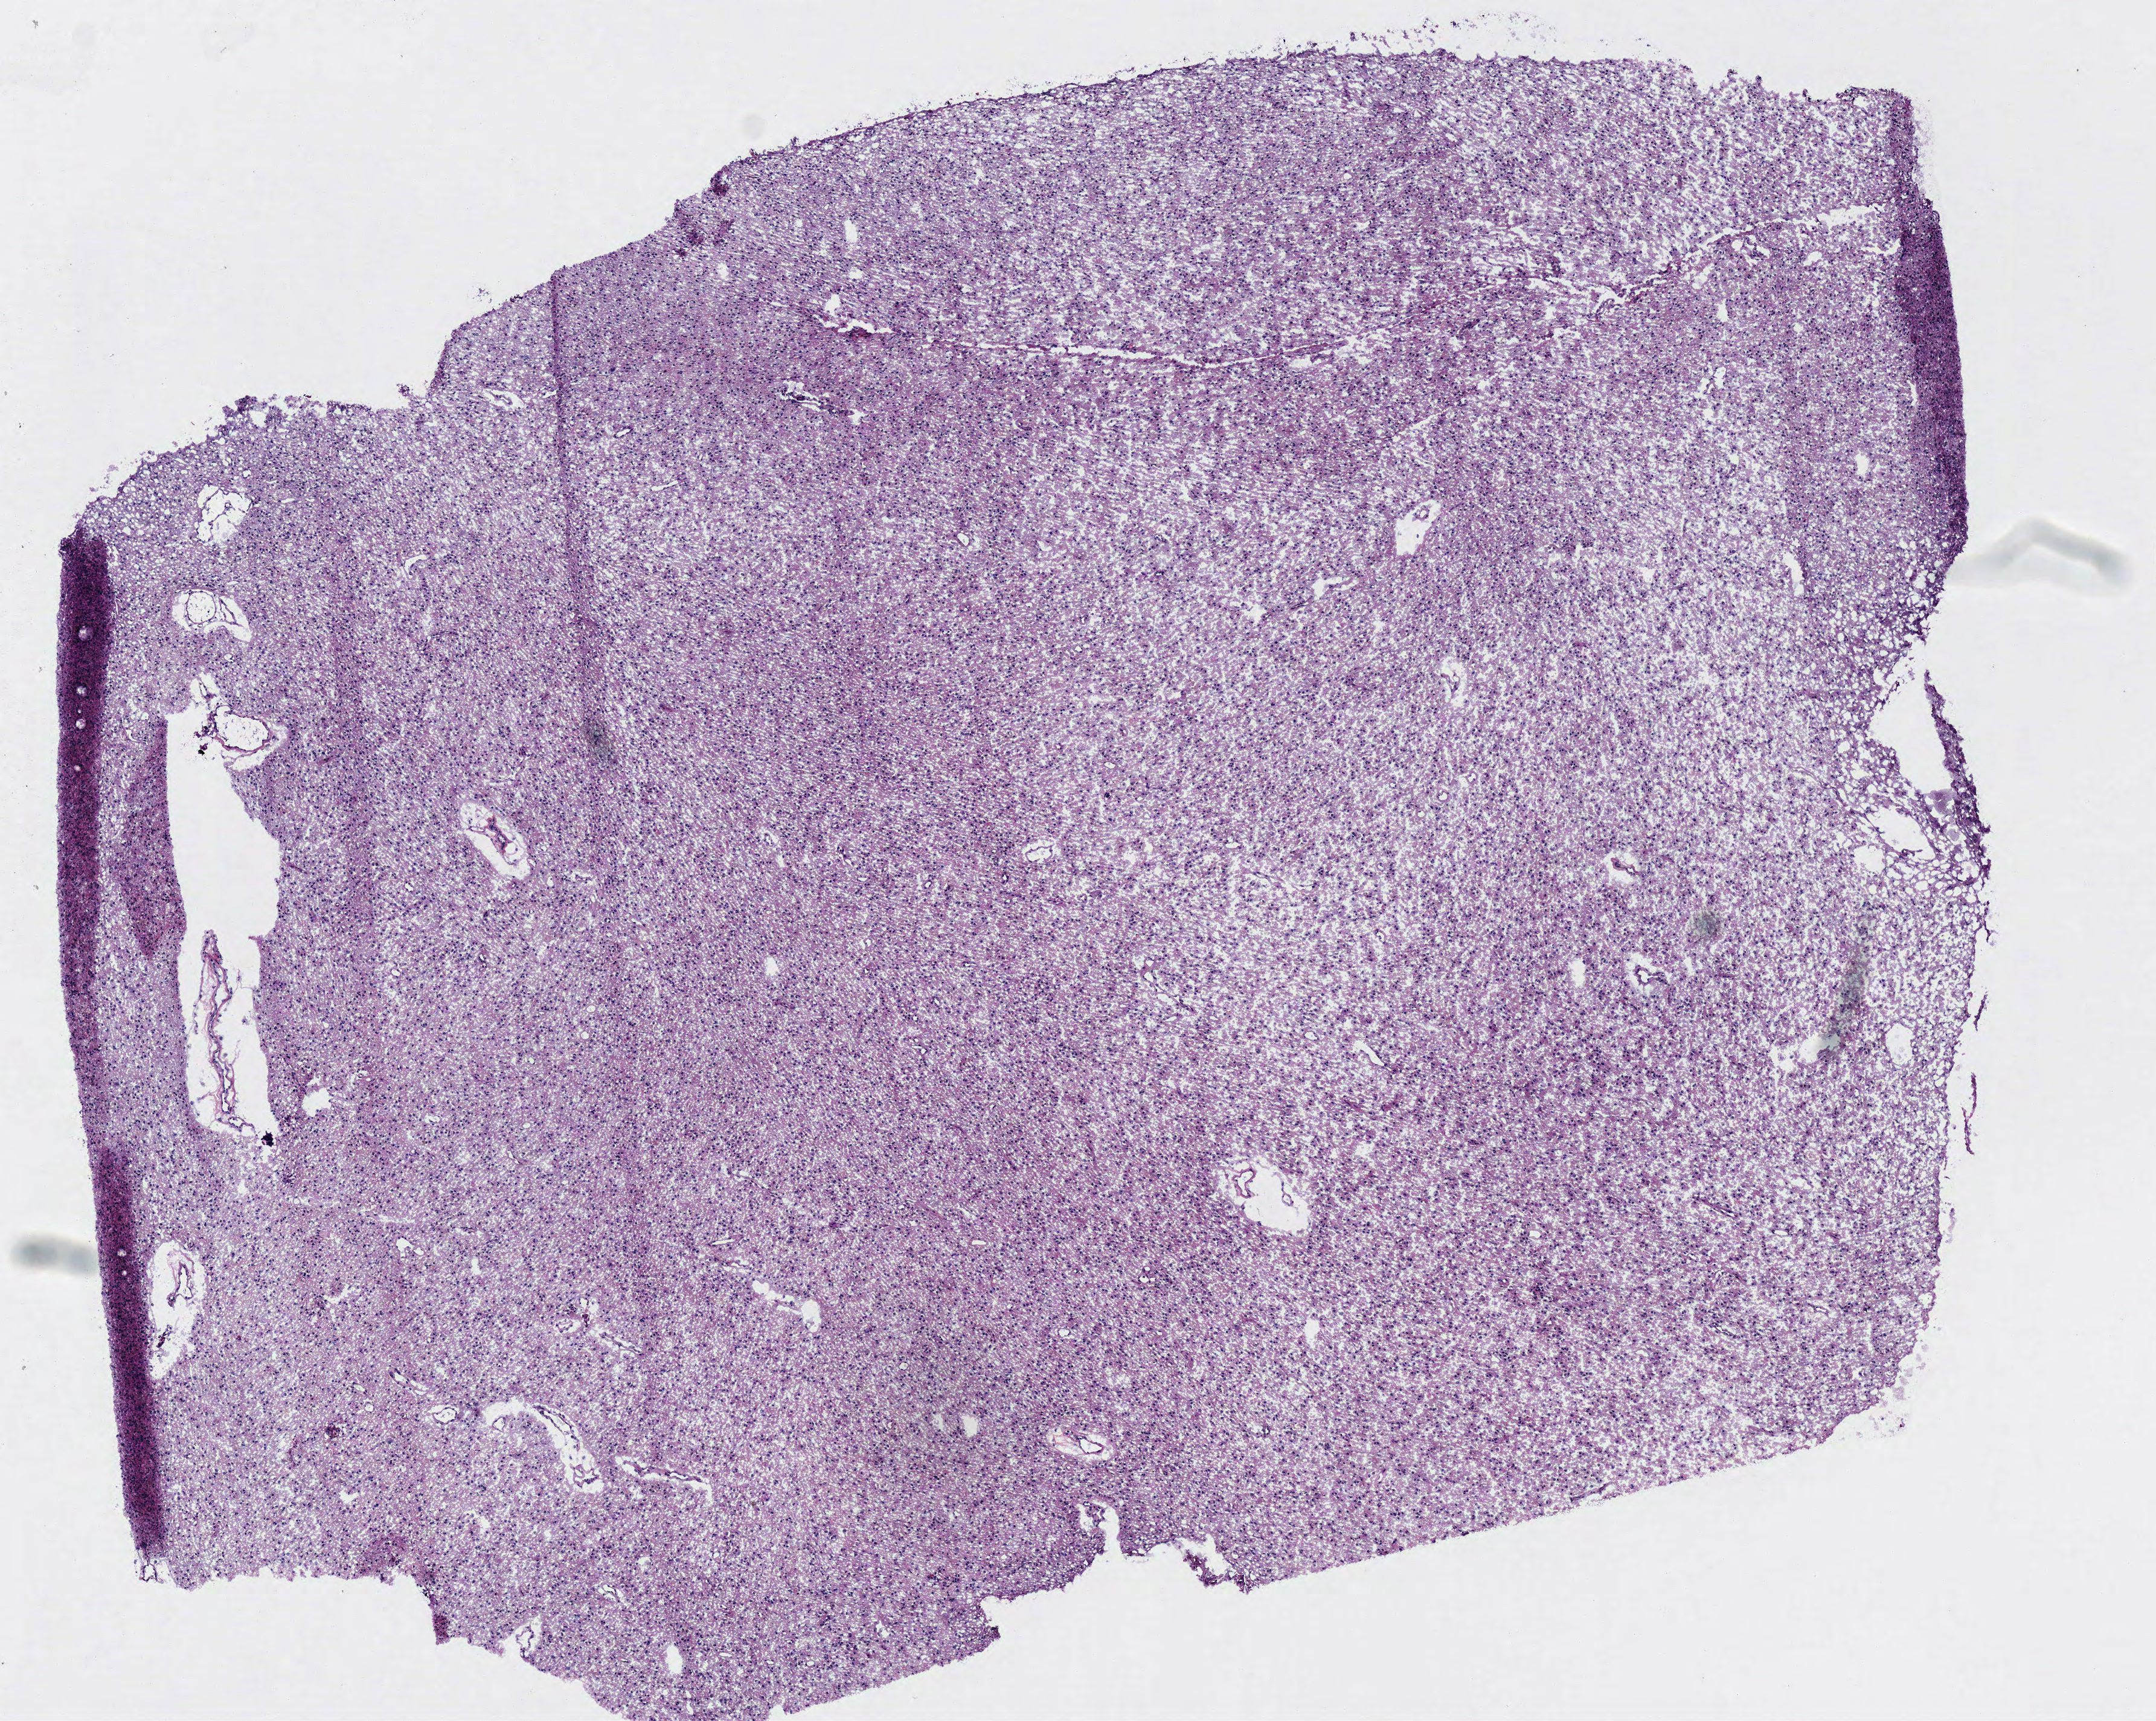
Digitized H&E-stained tissue section (whole slide), whole scanned area (about 7.0 x 5.6 mm) shown as a low-resolution overview; frozen section from the bottom of the tissue portion; sample: primary tumour, brain. Female patient; age at initial diagnosis 34 years. Histologic grade: G2 (moderately differentiated). Pathologist review of this section (percent, as recorded): tumour cells 100%, tumour nuclei 75%, normal cells 0%, stromal cells 0%, necrosis 0%.
Histologic diagnosis: Oligodendroglioma, NOS. Laterality: right.